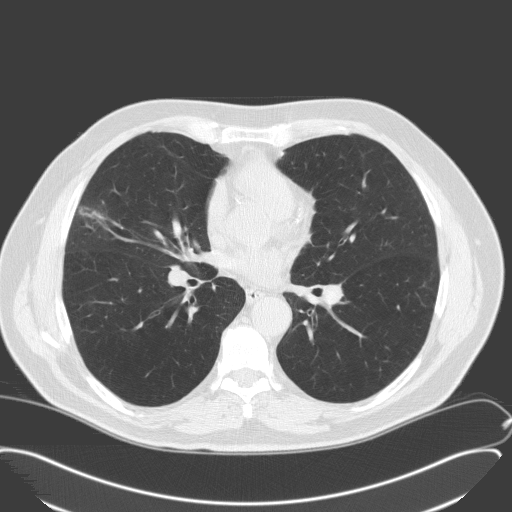
Chest CT (low-dose screening protocol), one axial image, second screening round (one year after baseline), lung window (W 1500 / L -600 HU), standard (soft-tissue) reconstruction kernel (C), slice 86 of 175 in the series. Male participant, aged 65 years at enrolment. Former smoker at enrolment.
Lesion marked by an expert reader, bounding box <59,192,116,245> (left, top, right, bottom; pixels). Screening reader's record for this exam: no non-calcified nodule ≥4 mm recorded. Official screen result: negative screen, minor abnormalities not suspicious for lung cancer. Lung cancer was diagnosed 346 days after this screen: adenocarcinoma, NOS, right middle lobe, moderately differentiated (G2), stage IA (AJCC 6th edition), 25 mm at pathology.